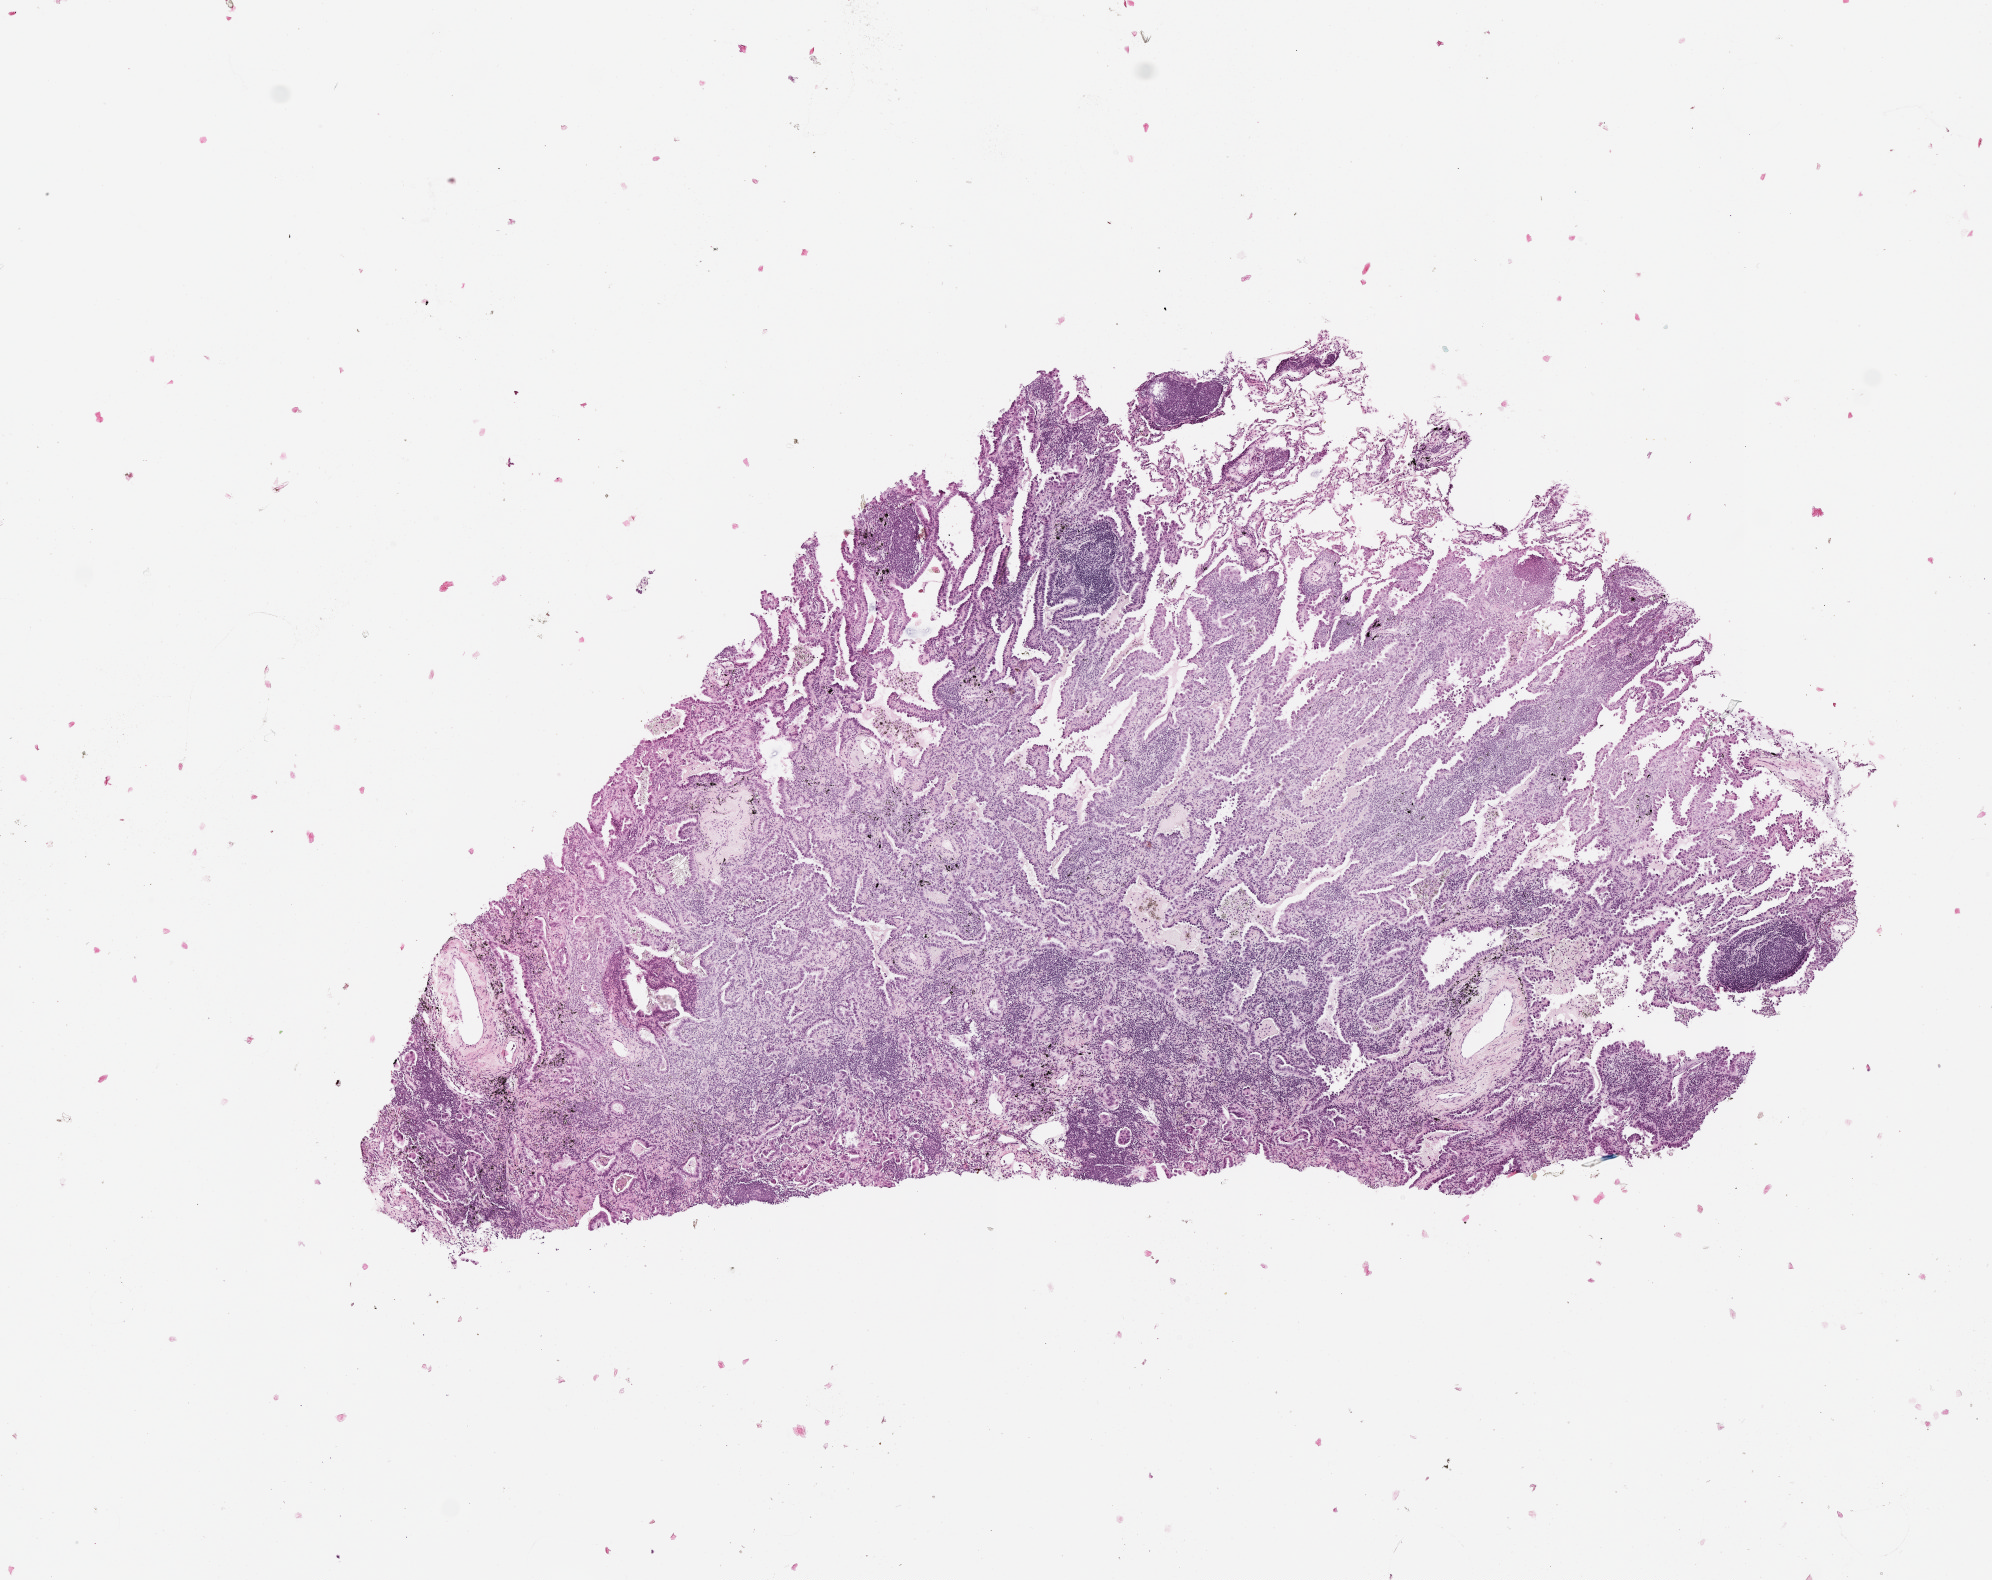
Digitized H&E-stained tissue section (whole slide) — low-resolution overview of the scanned area, about 8.0 x 6.4 mm, lung, tissue type not recorded.
Patient diagnosis (cohort enrolment): lung adenocarcinoma (lung).